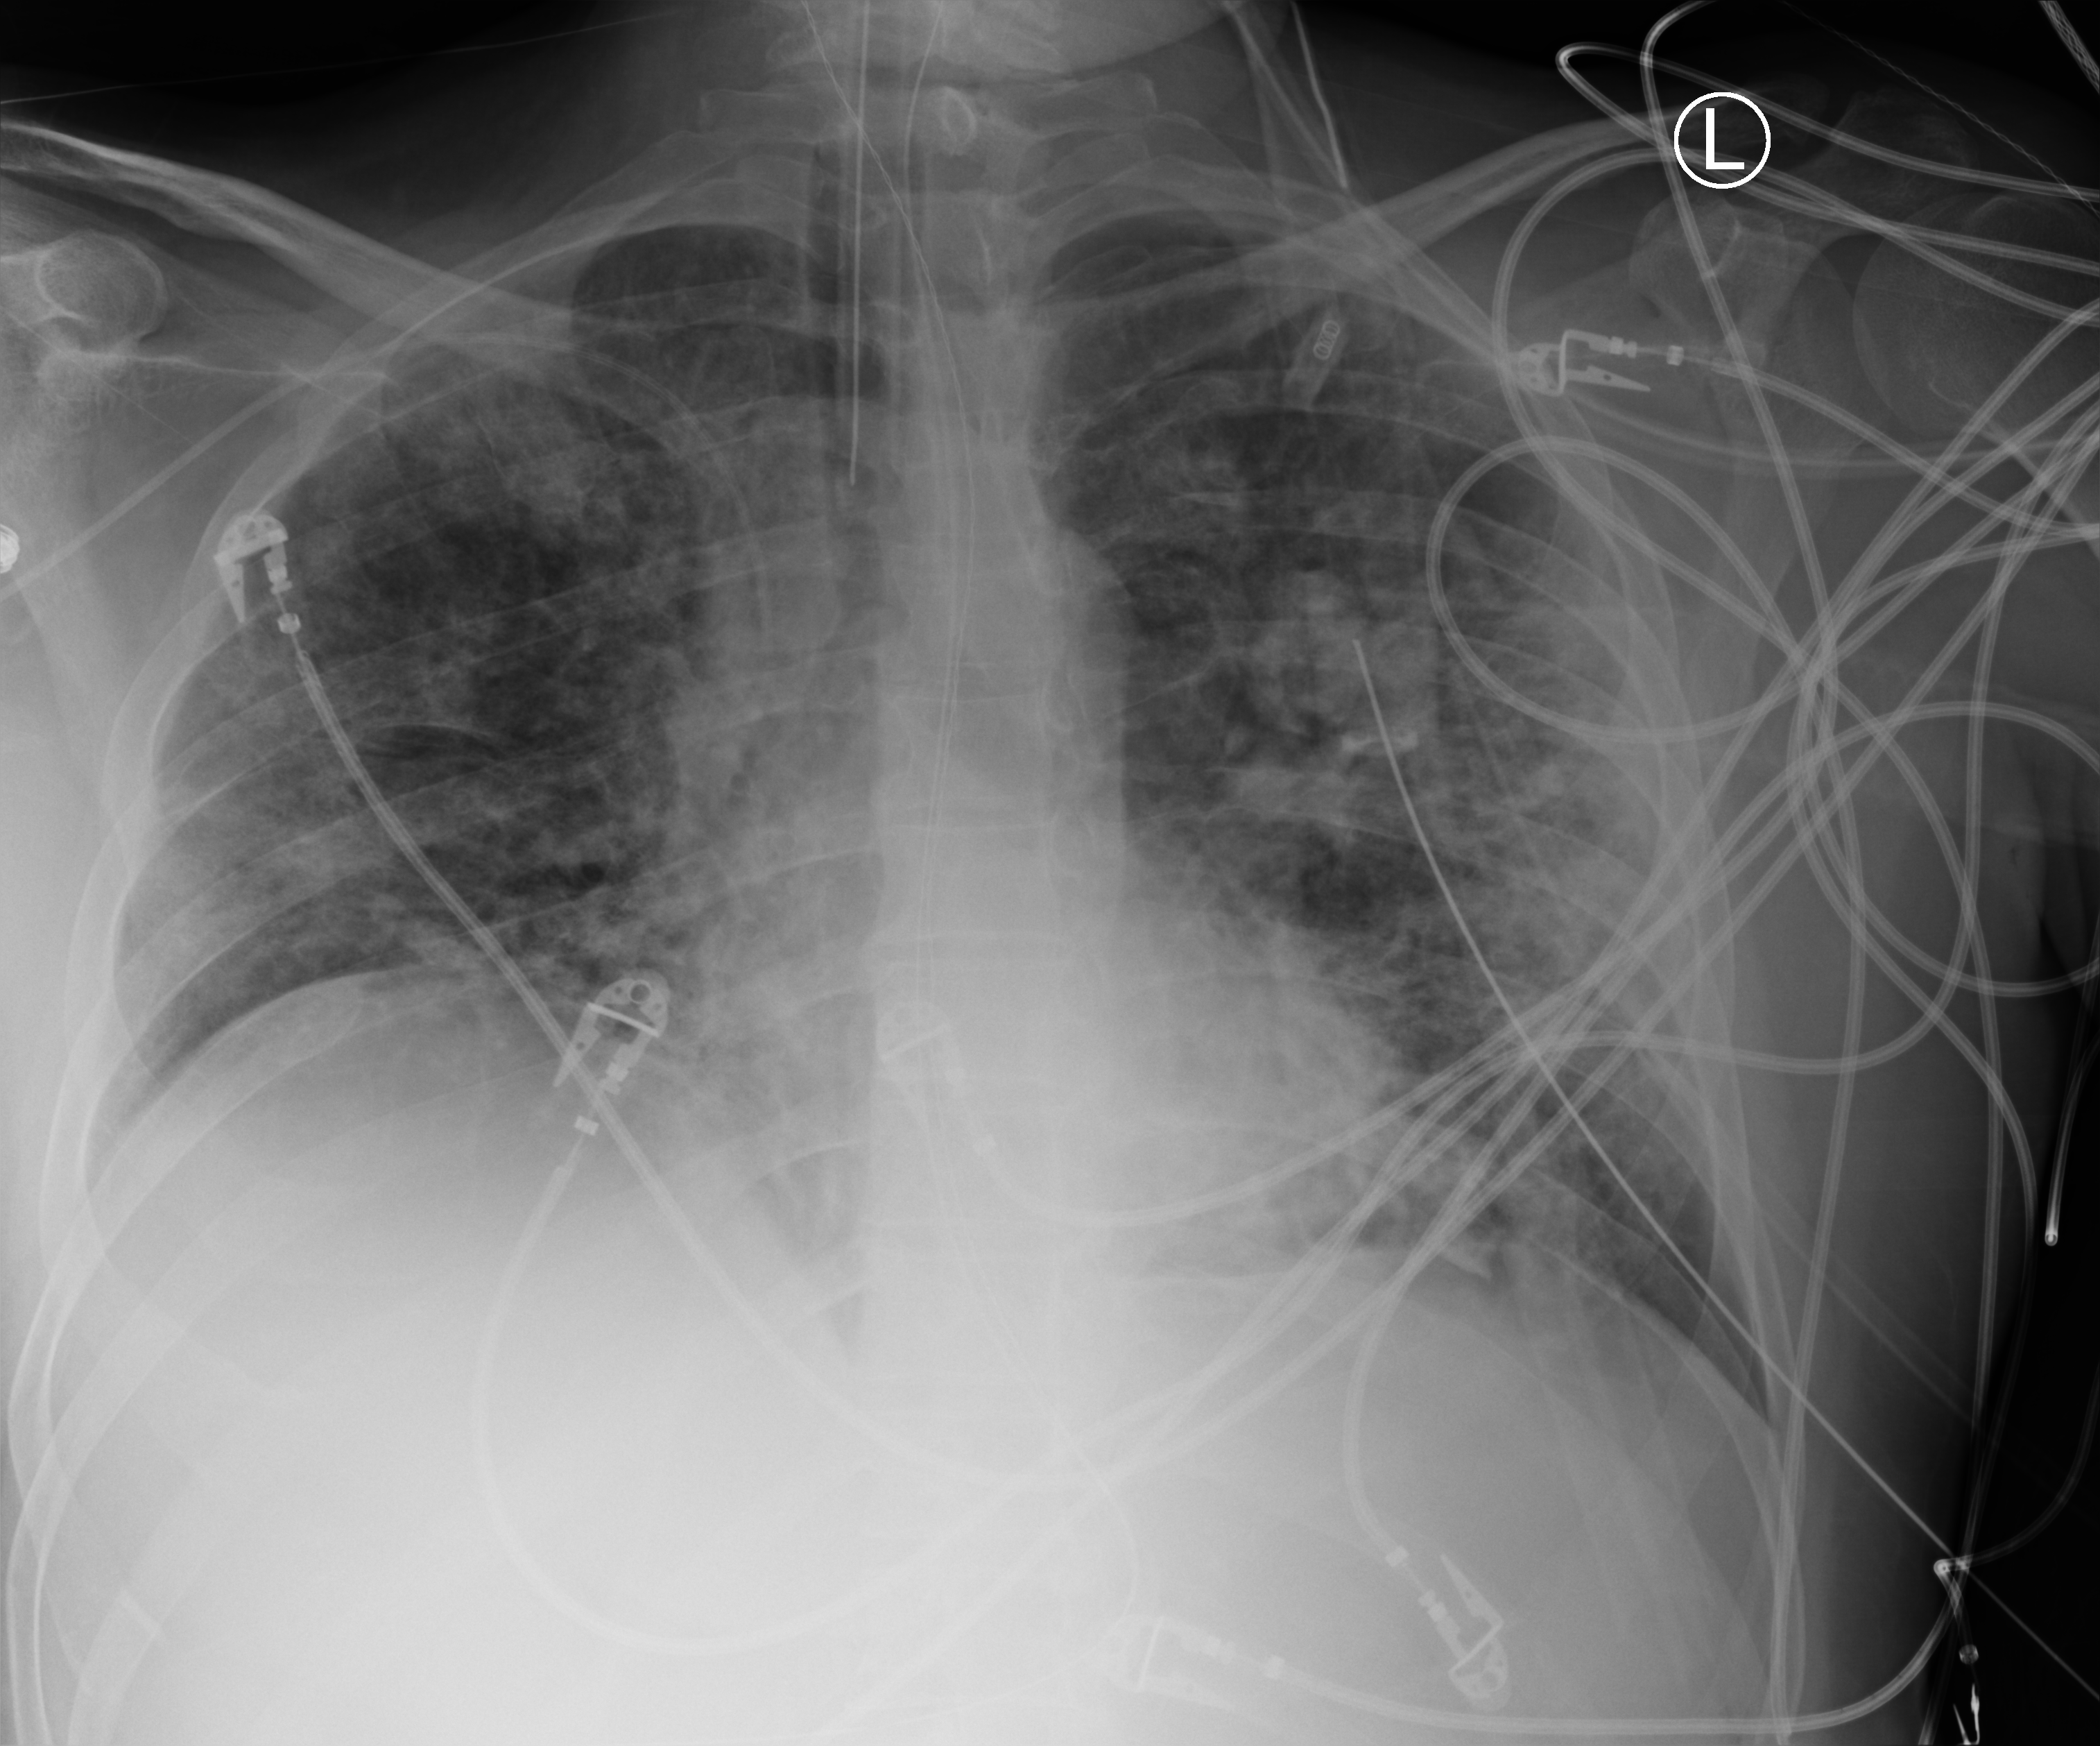
Portable chest radiograph, anteroposterior (AP) projection. Patient hospitalised with COVID-19; male, aged 18–59 years.
From the hospital-stay record, not from the radiograph (when in the stay this image was taken is not recorded): length of hospital stay: 48 days.